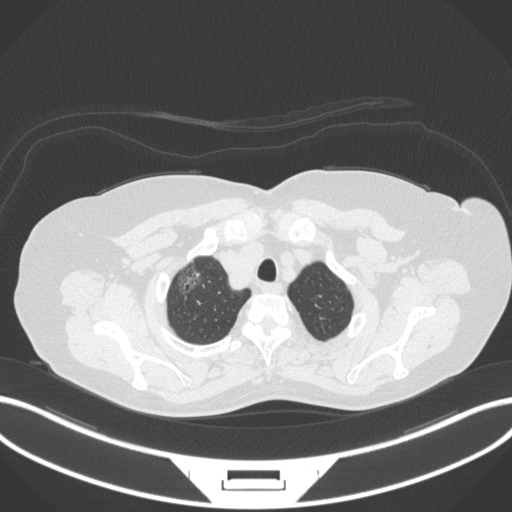
Chest CT, one axial slice. Slice 312 of 365 in the series (ordered by position). Reconstruction kernel B31f. Lung window (W 1500 / L -600 HU). 1 mm slice thickness. 512 × 512 image matrix, field of view 400 × 400 mm. Patient: female, 62 years. Case-level facts recorded for this patient, not image findings: clinical TNM (as recorded): T1c N0 M0.
Structures marked on this image (rectangle marked by the reading radiologist):
- lung tumour (recorded histology: adenocarcinoma): bounding box (x1, y1, x2, y2) in pixels: (176, 264, 205, 298)